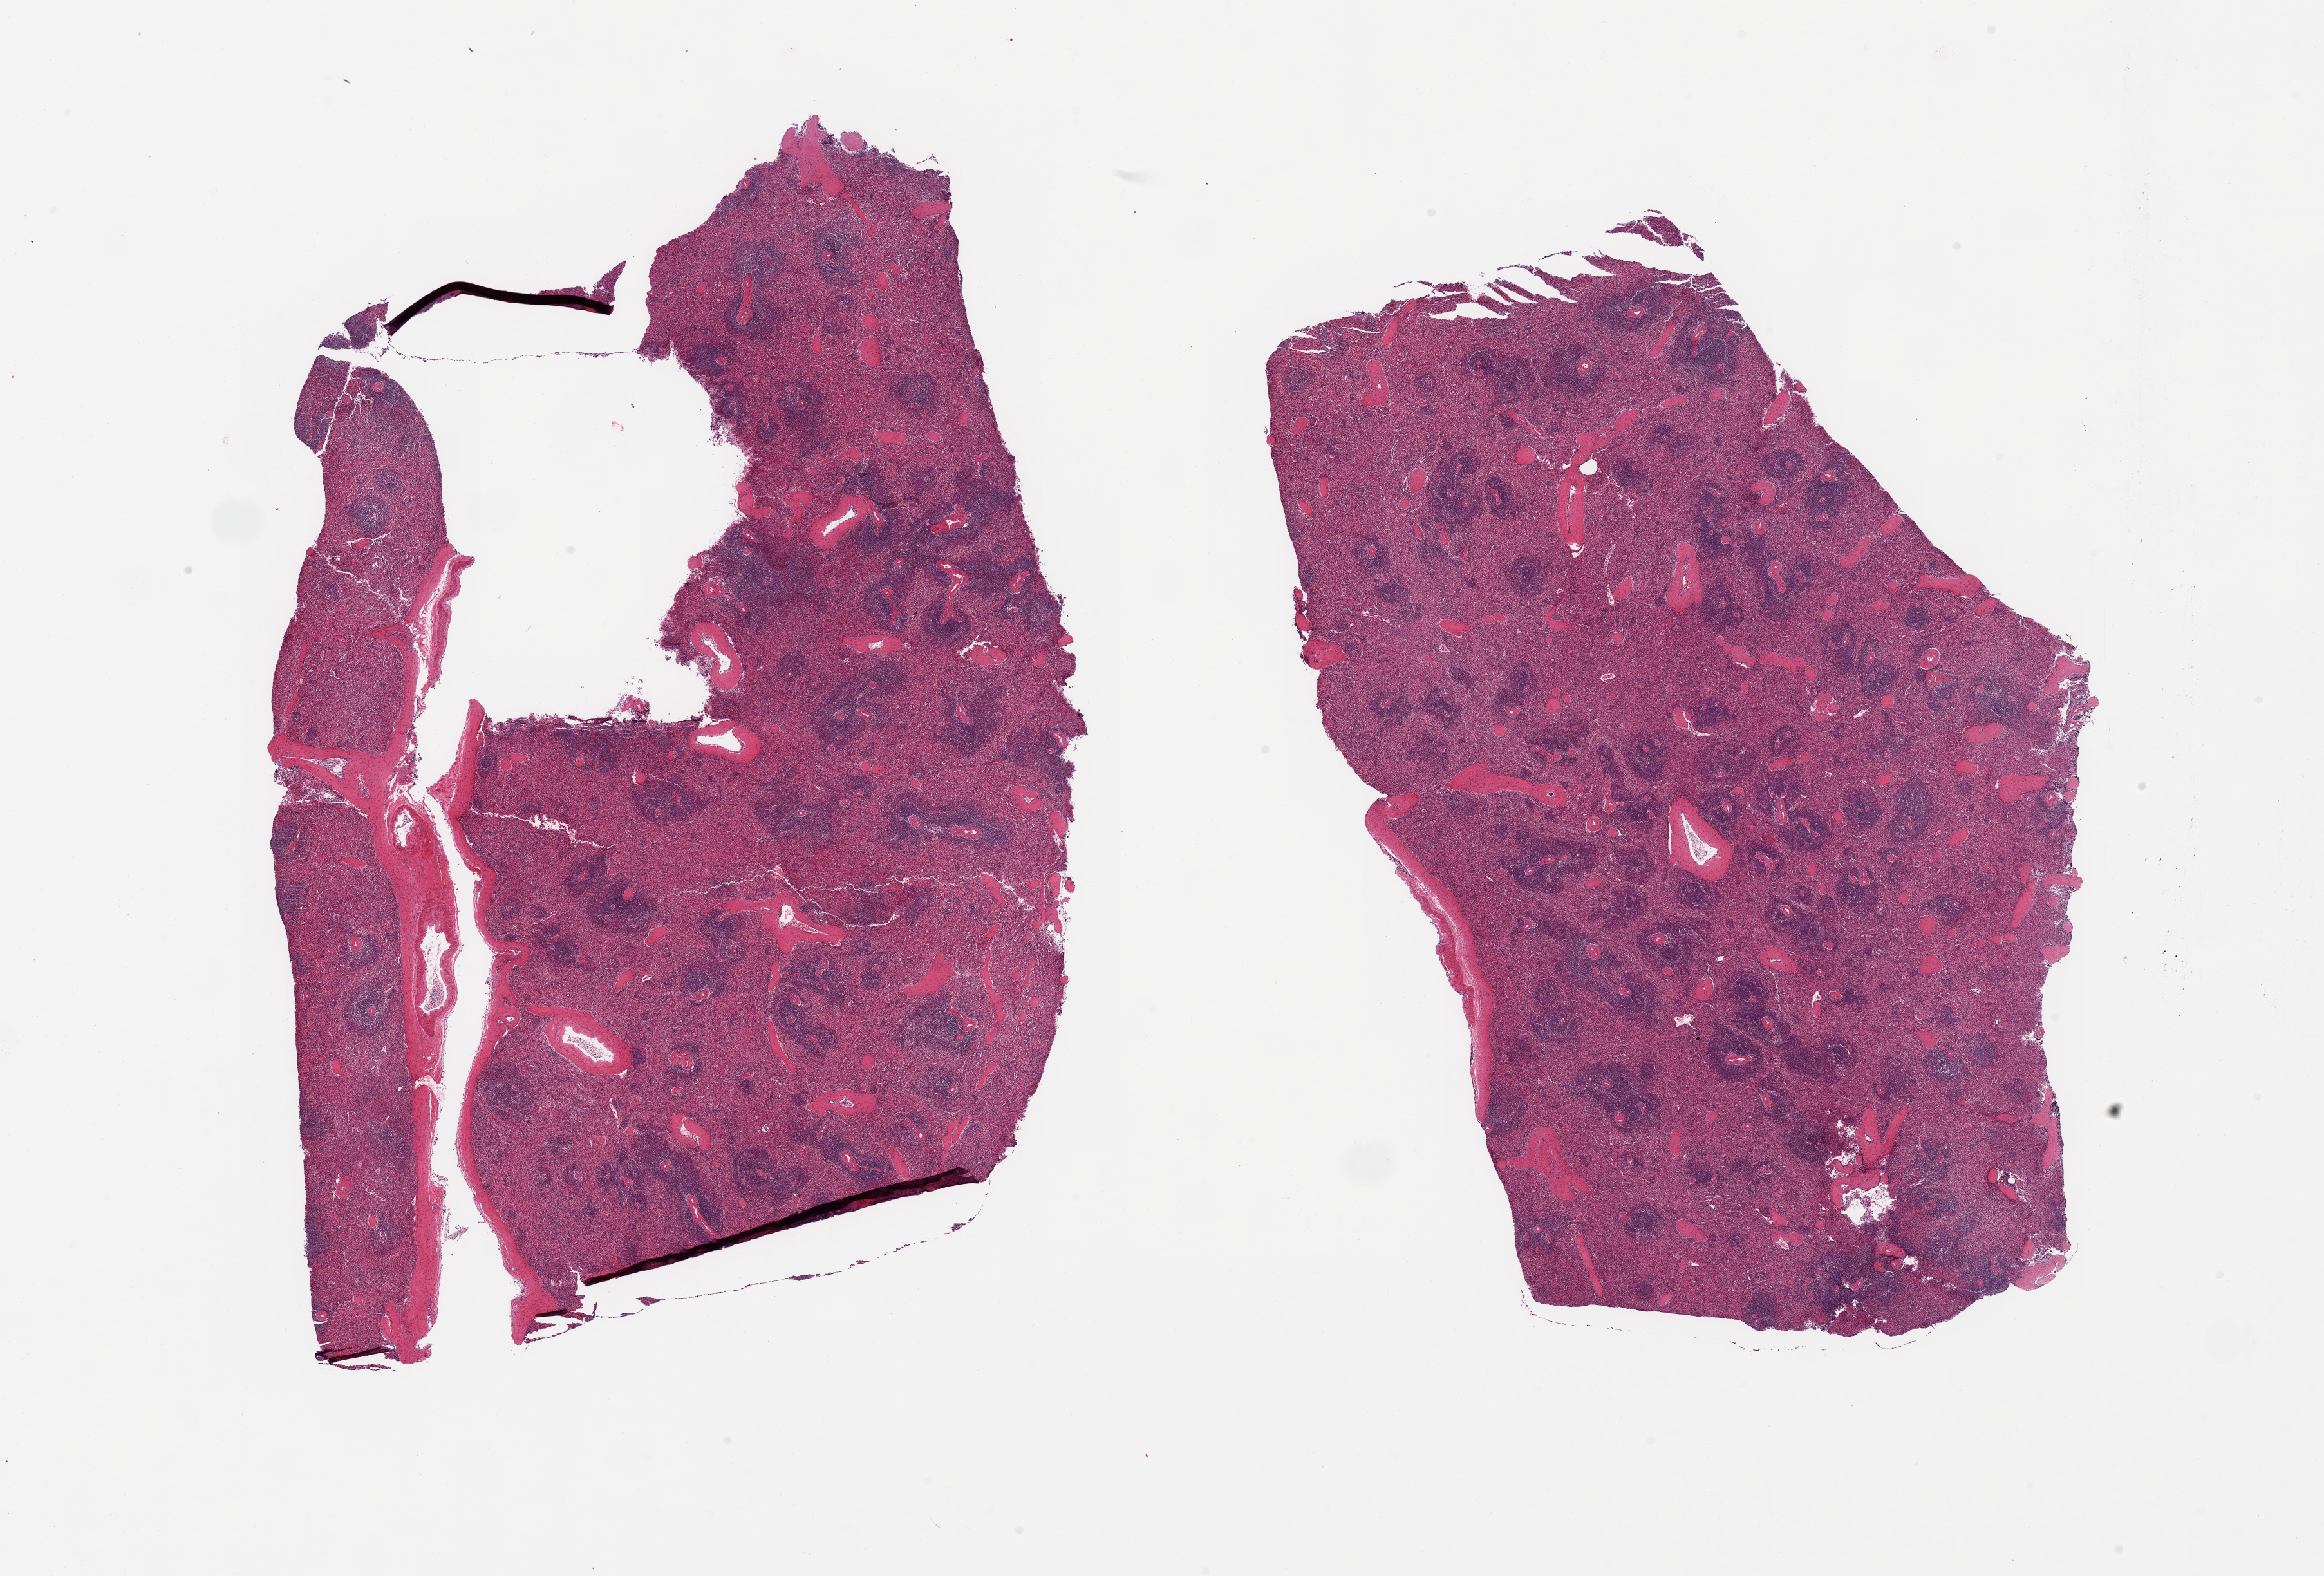
Haematoxylin and eosin whole-slide image, shown as a low-resolution overview of the whole scanned area (about 28.5 x 19.4 mm), PAXgene-fixed, paraffin-embedded tissue, target tissue: spleen, donor tissue sample.
Pathologist's review note for this sample: 2 pieces; mild congestion.